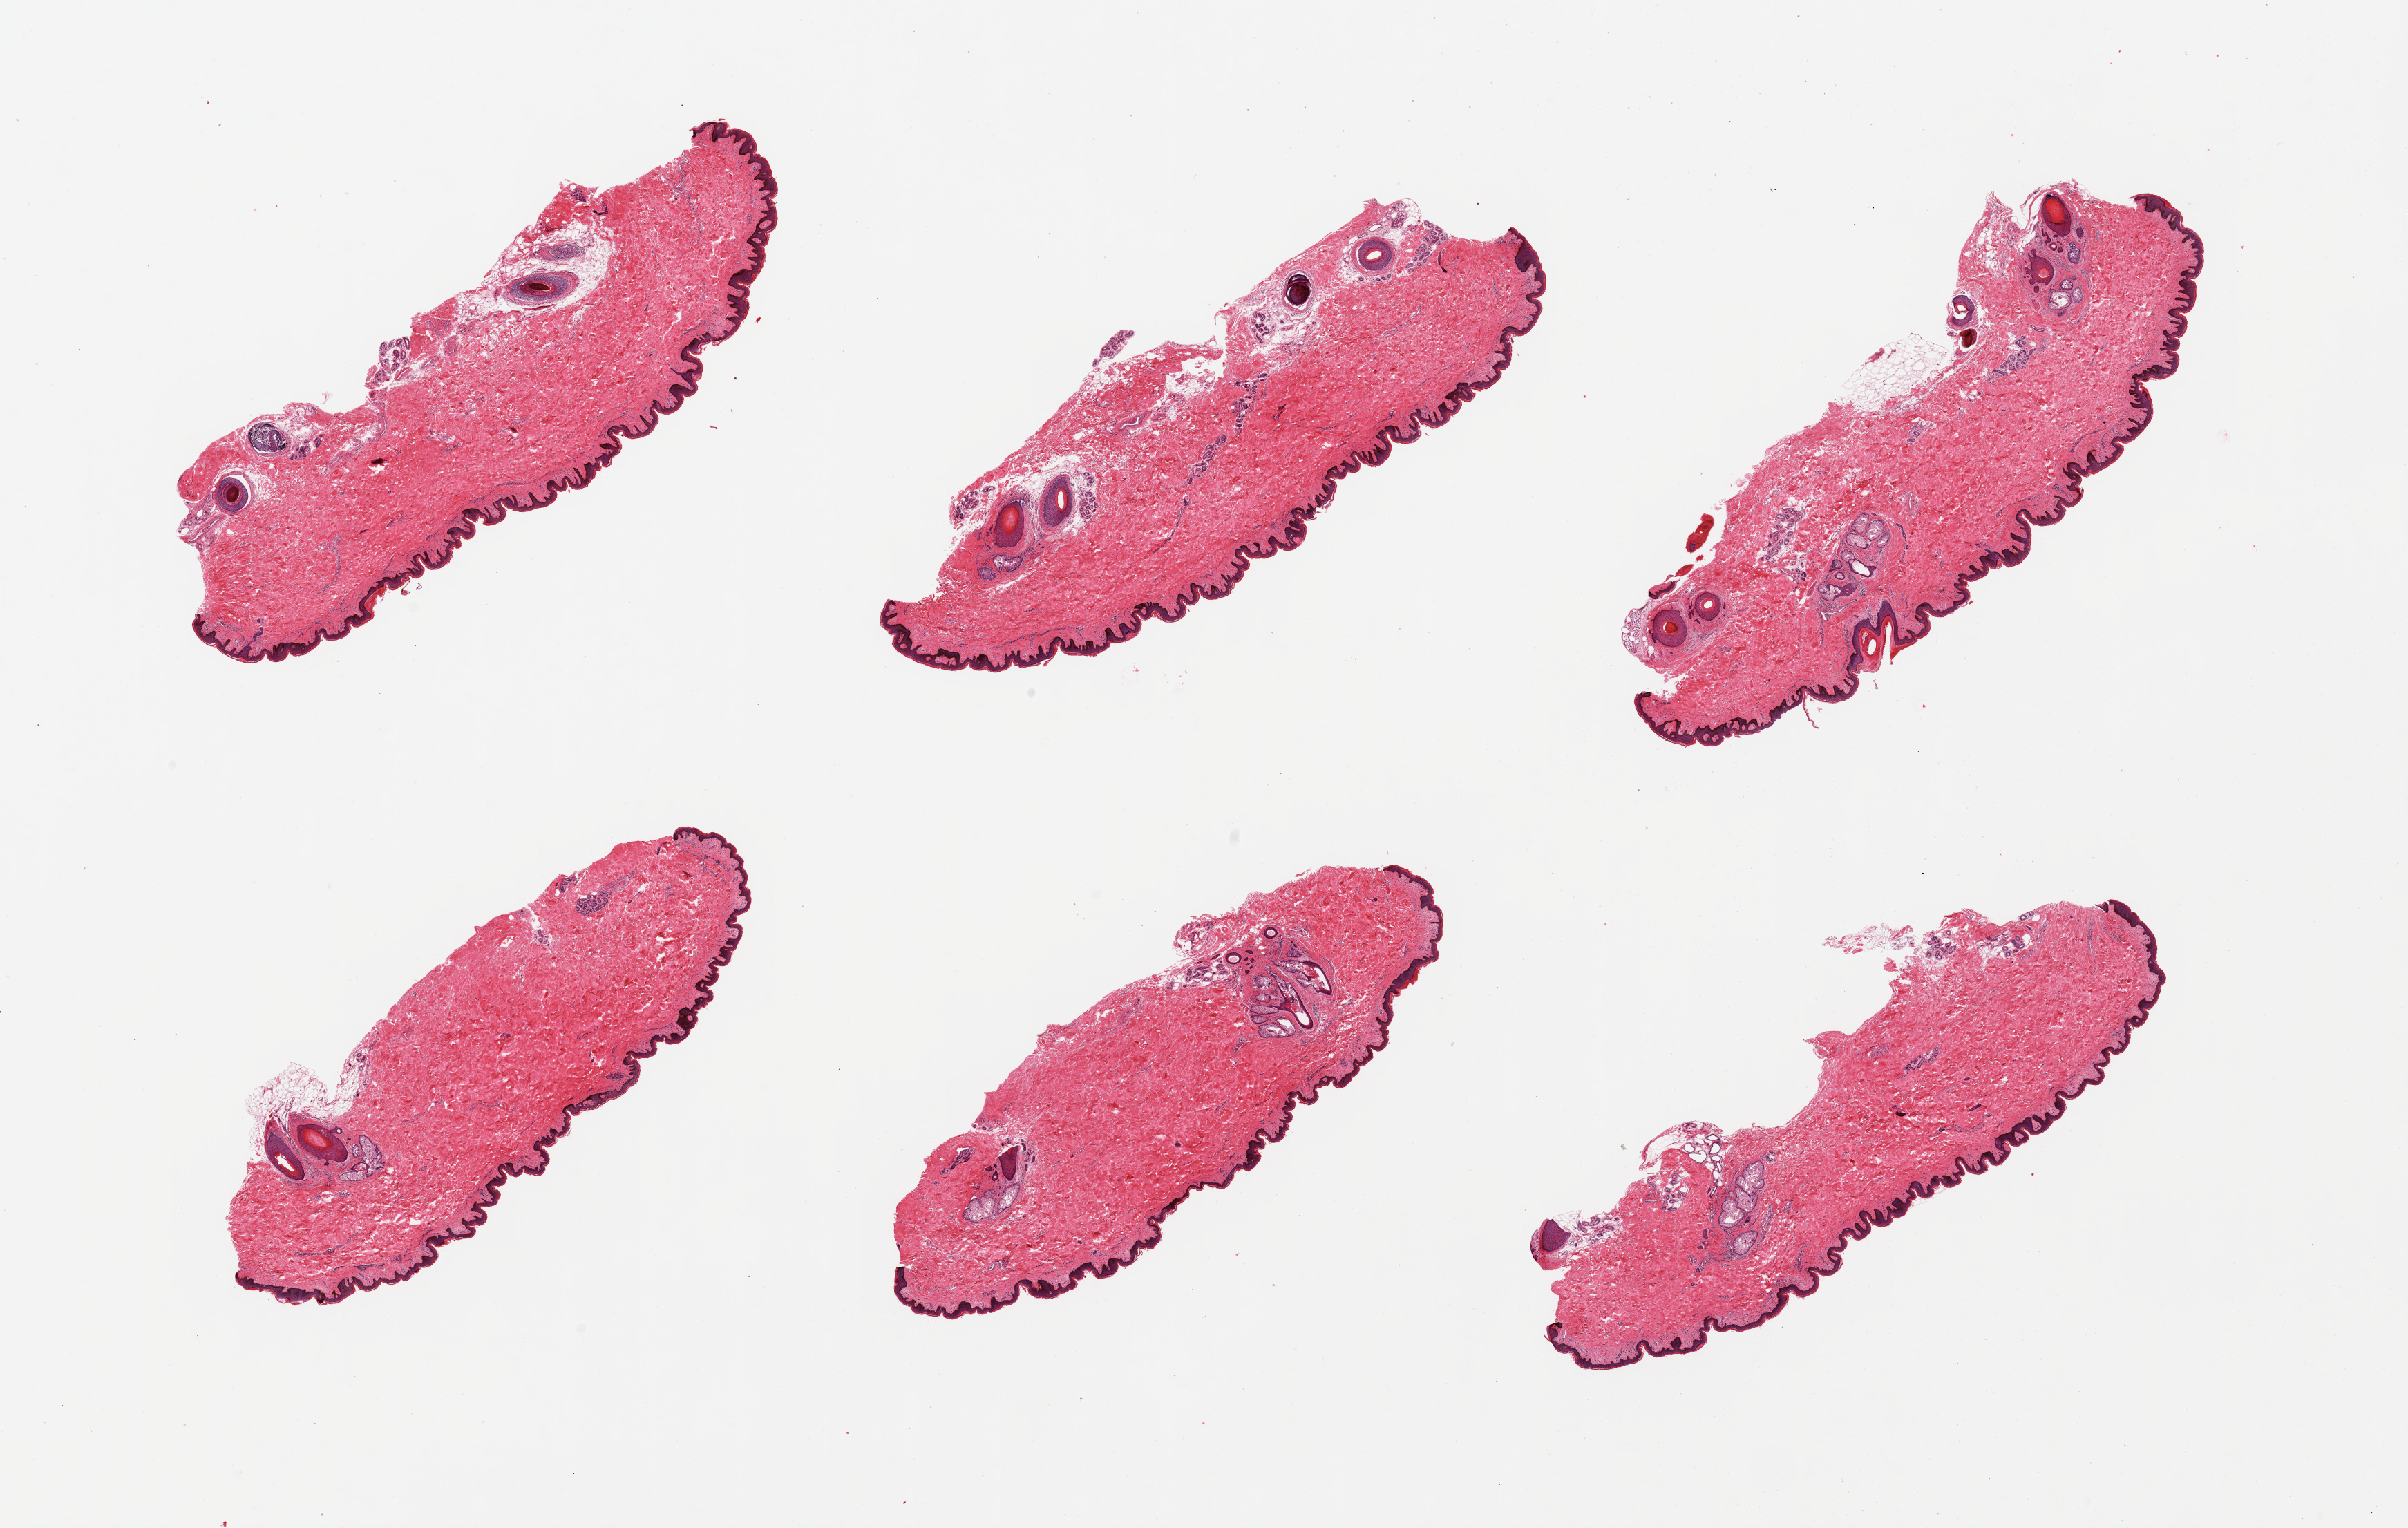
Hematoxylin and eosin (H&E) whole-slide image, whole scanned area (about 27.6 x 17.5 mm, acquisition: 20x scan) shown as a low-resolution overview; PAXgene-fixed paraffin-embedded (PFPE) section; target tissue: skin of suprapubic region; donor tissue sample.
Reviewer comment on this tissue sample: 6 pieces; up to 4 hair follicles per piece; well trimmed.